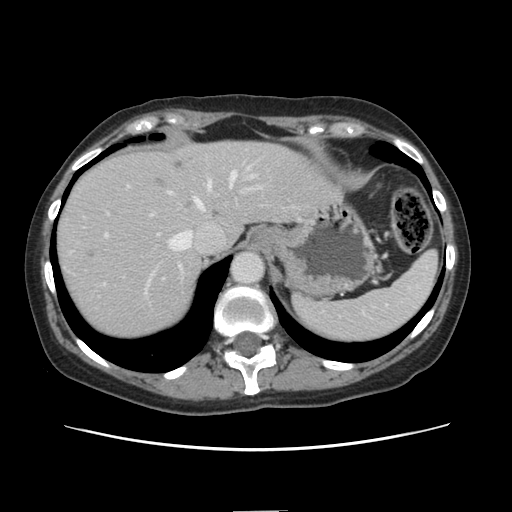
Contrast-enhanced abdominal CT, one axial slice; position 113 of 141 along the scan axis; 120 kVp; intravenous contrast given; soft-tissue window (W 400 / L 40 HU); 512 × 512 image matrix, field of view 350 × 350 mm. Female patient, age 63 years. Case-level facts recorded for this patient, not image findings: diagnosis: colorectal cancer liver metastases, imaged before liver resection; multiple liver metastases: yes; largest metastasis: 3.2 cm; chemotherapy before resection: yes.
Annotated regions visible in this slice (manually delineated by an expert):
- hepatic veins: bounding box (x1, y1, x2, y2) in pixels: (147, 172, 236, 287)
- liver: (57, 141, 335, 340)
- planned liver remnant (the part of the liver to remain after resection): (195, 142, 338, 241)
- portal vein (with intrahepatic branches): (237, 164, 252, 175)
- liver metastasis: (152, 177, 163, 187)